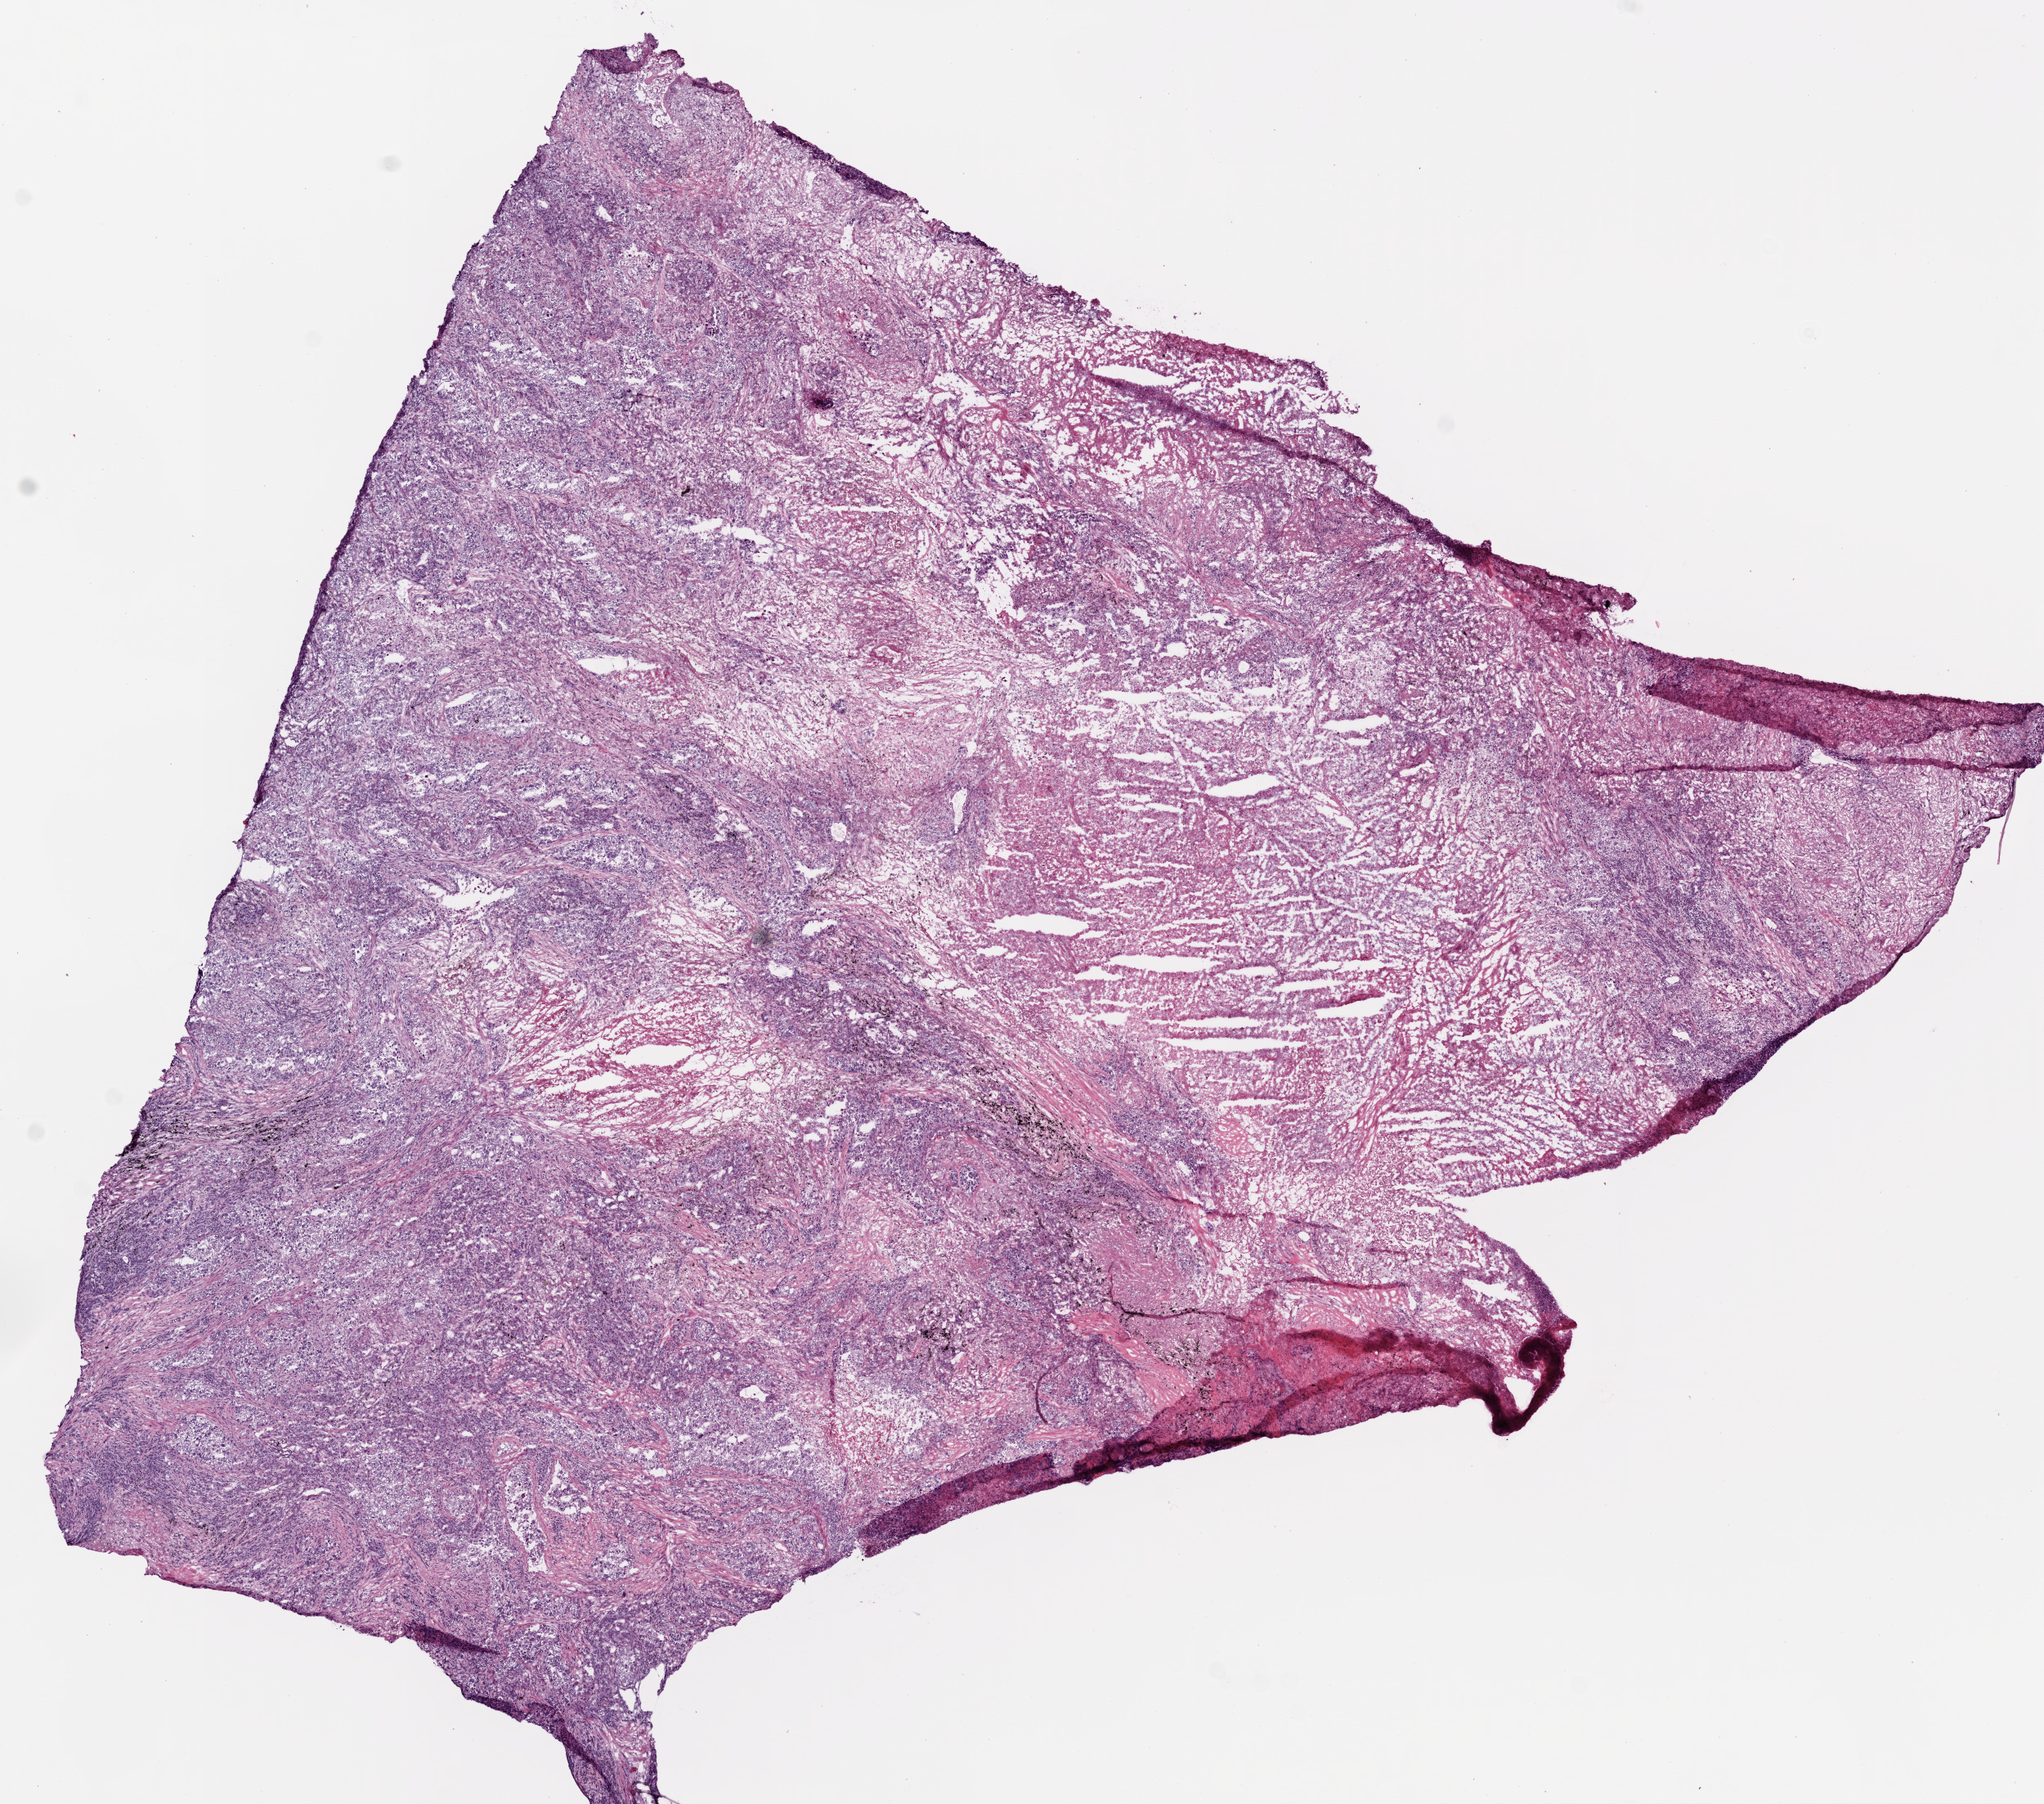
Whole-slide histology image, H&E — a low-resolution overview of the entire scanned area, about 10.0 x 8.9 mm; frozen section from the top of the tissue portion; primary tumour sample from the lung. Patient: male, age at initial diagnosis 68 years. Pathologist review of this section (percent, as recorded): tumour nuclei 70%, normal cells 0%, stromal cells 10%, necrosis 20%.
Laterality: left. TNM: T2 N0 M0. Diagnosis: Adenocarcinoma with mixed subtypes (upper lobe, lung). AJCC pathologic stage: IB (6th edition).